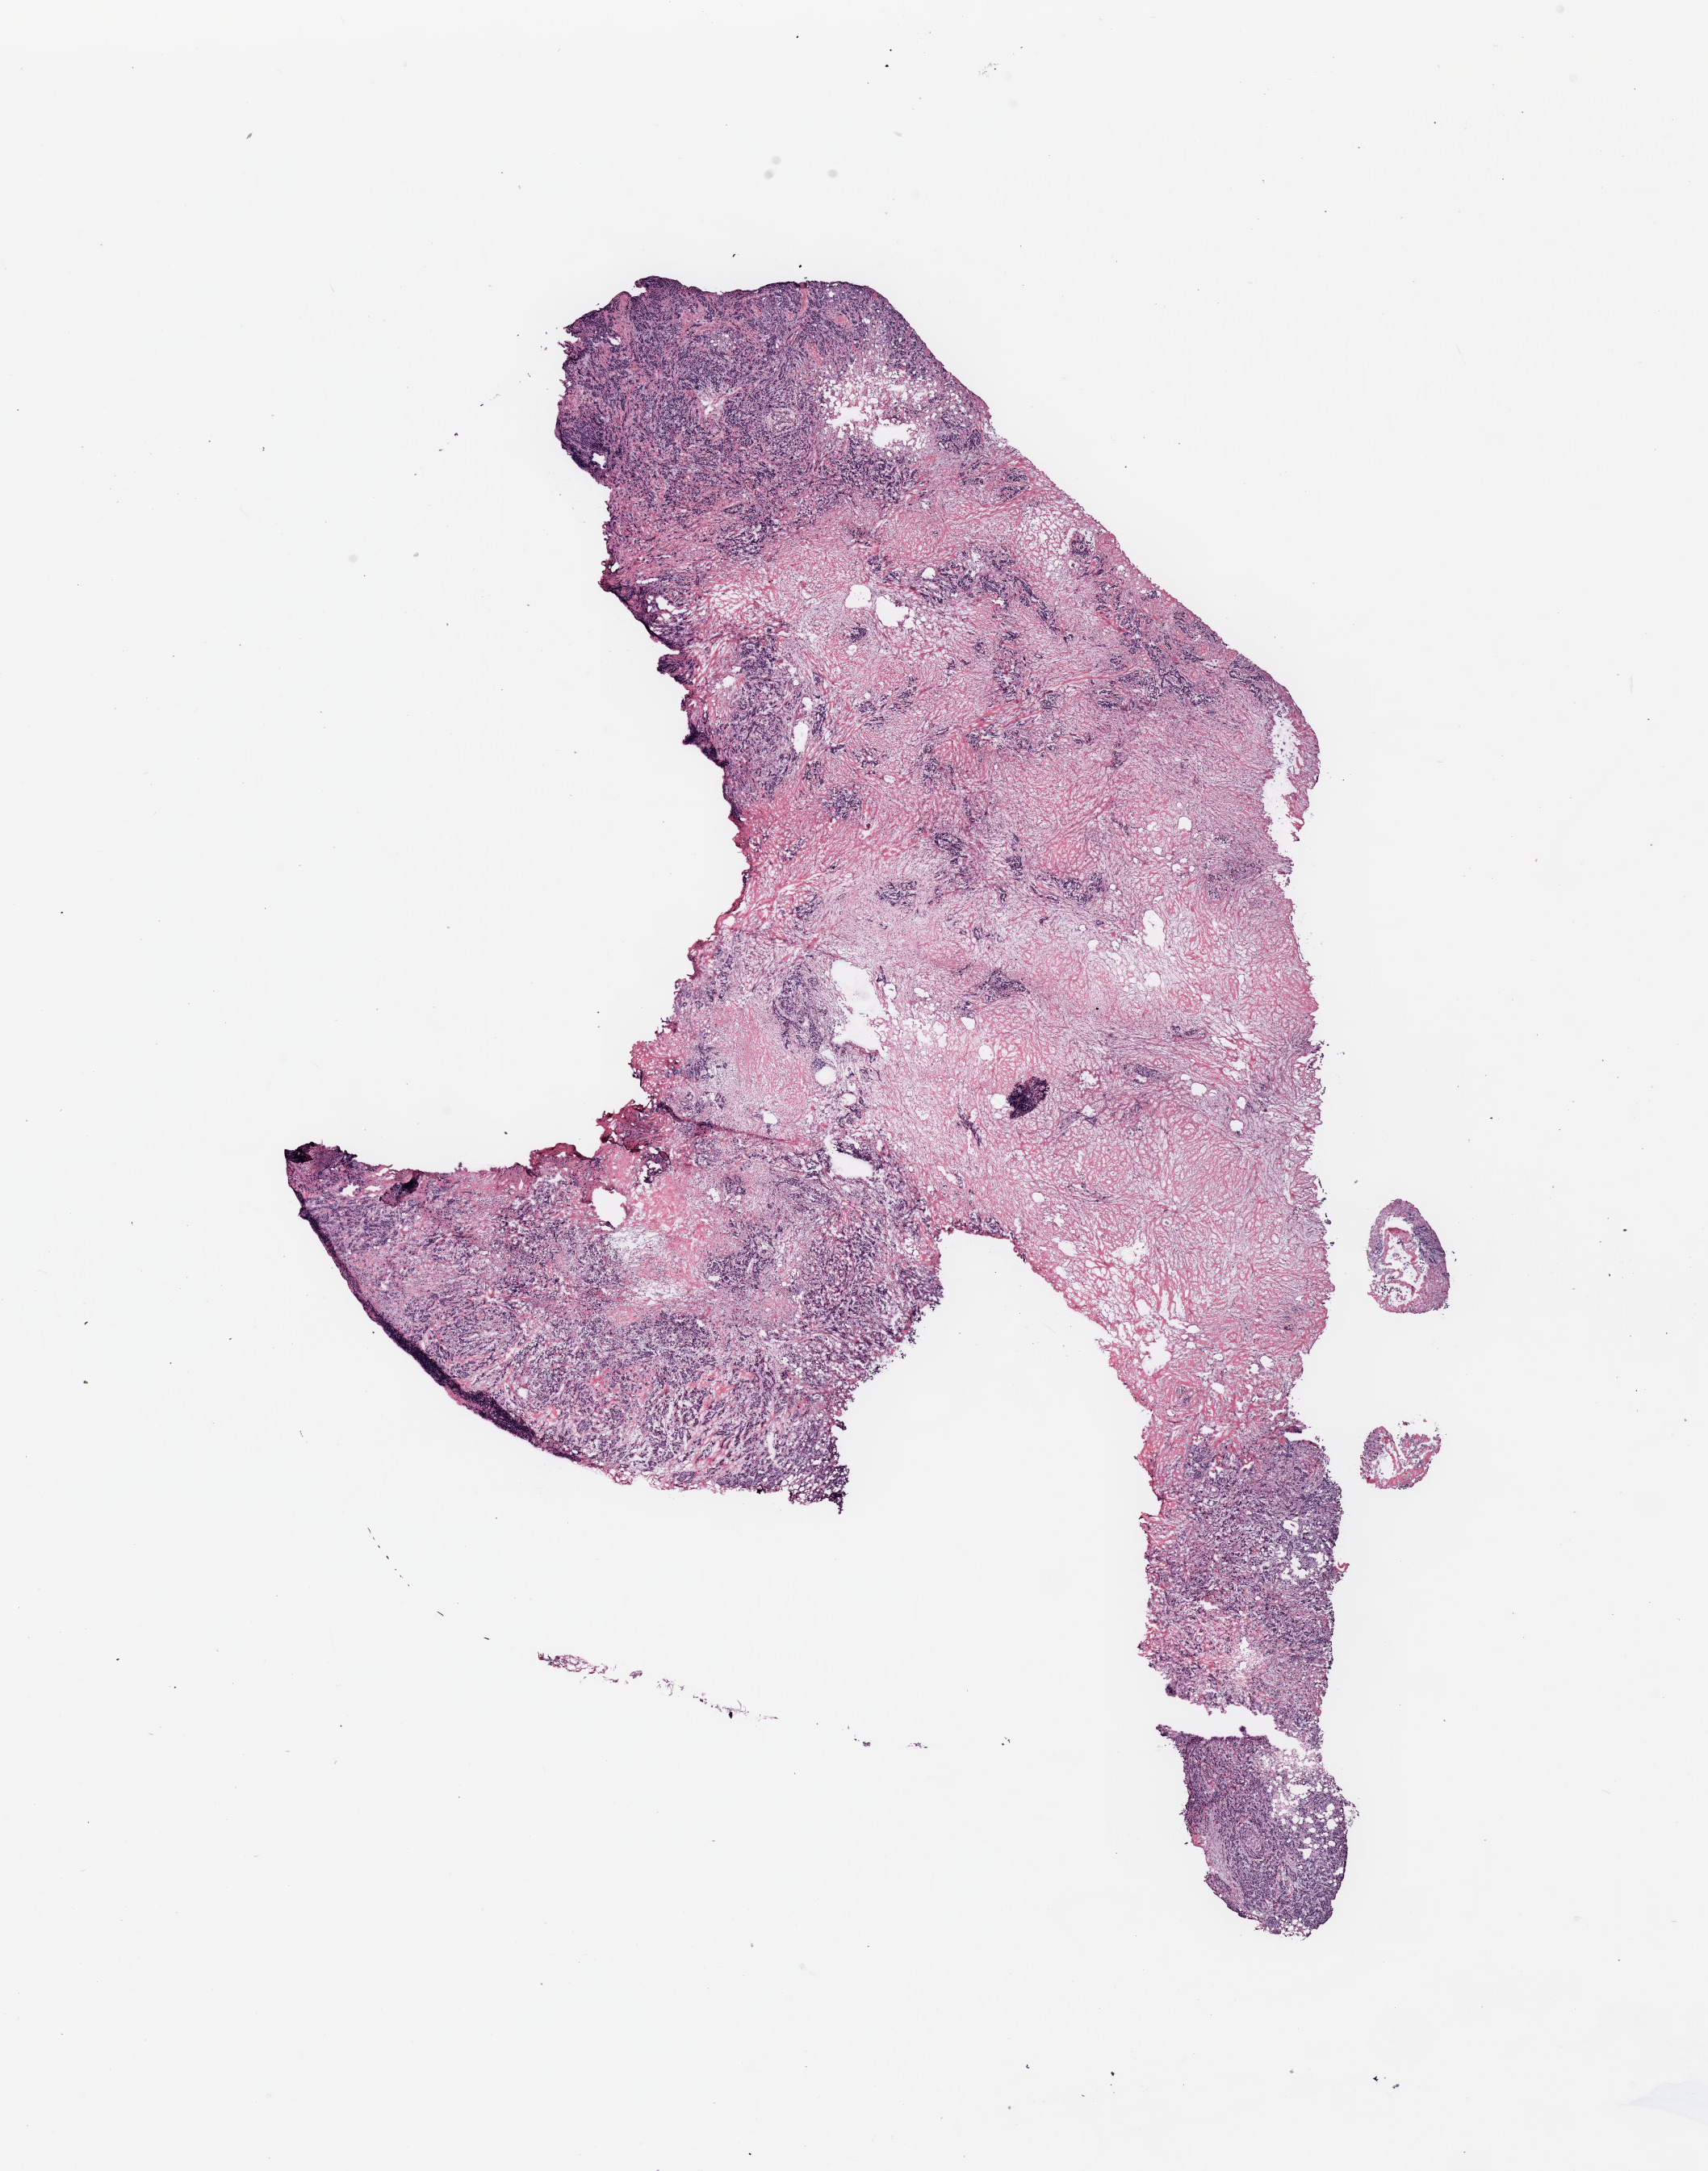
Whole-slide histology image, Hematoxylin and eosin (H&E) stained, a low-resolution overview of the entire scanned area, about 16.7 x 21.3 mm; breast, tumour tissue. Patient: female, age 46 years.
AJCC pathologic stage: IIB. Diagnosis: Infiltrating duct and lobular carcinoma.